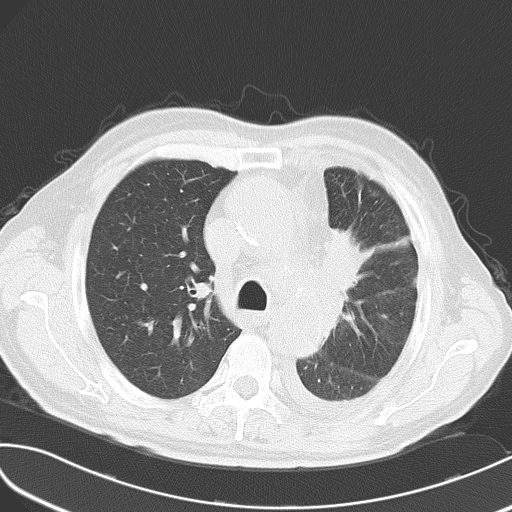
Chest CT, one axial slice. Position 38 of 54 along the scan axis. Reconstruction kernel B70f. Lung window (W 1500 / L -600 HU). 5 mm slice thickness. 512 × 512 image matrix. Patient: male, 70 years. Case-level facts recorded for this patient, not image findings: clinical TNM (as recorded): T2 N1 M3; histopathological grade: G3.
Annotated regions visible in this slice (bounding box drawn by a radiologist):
- lung tumour (recorded histology: small cell carcinoma): bounding box <322,208,375,300> (left, top, right, bottom; pixels)